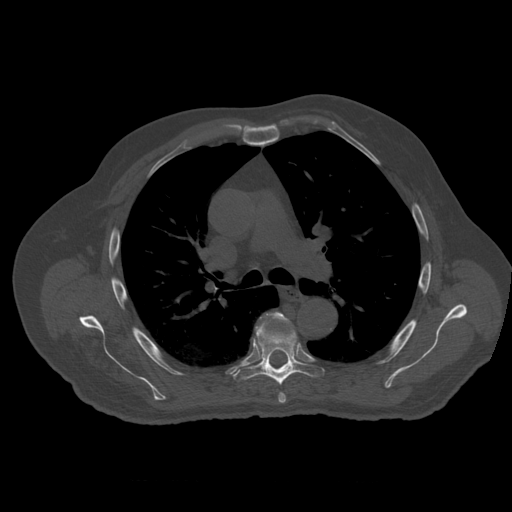
CT including the spine, one axial slice; 120 kVp; bone window (W 1800 / L 400 HU); 1.25 mm slice thickness; 512 × 512 image matrix. Patient age 73 years. From the clinical record (not read from this slice): primary cancer: prostate.
Annotated regions visible in this slice (semi-automatic segmentation, software-assisted and operator-edited):
- T5 vertebra: bounding box [x1, y1, x2, y2] px = [274, 313, 289, 404]
- T6 vertebra: [234, 319, 325, 385]